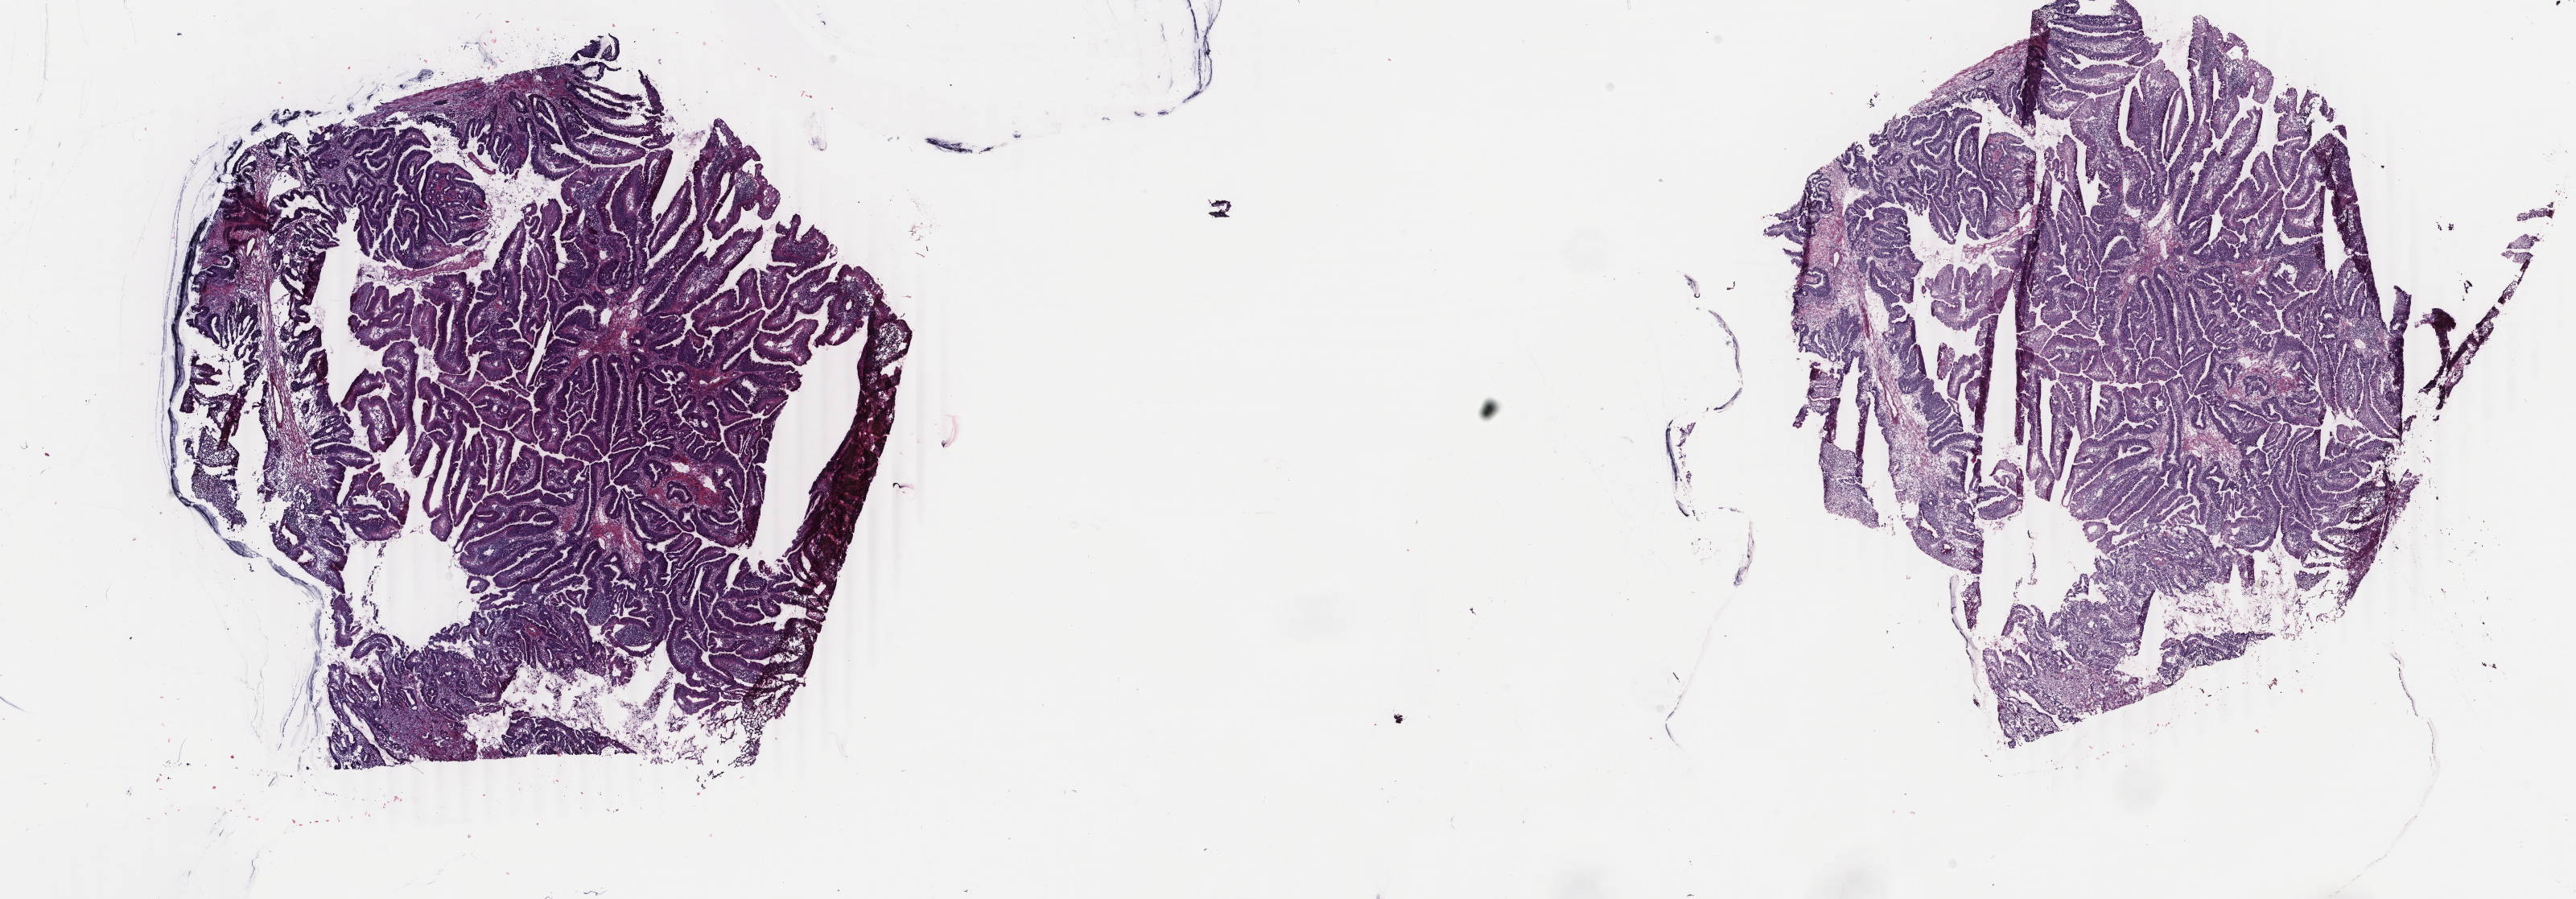
Whole-slide histology image, H&E-stained — low-resolution overview of the scanned area, about 25.5 x 8.9 mm (acquisition: 40x scan), frozen section, colon, primary tumour sample. Patient sex: female. Pathologist review of this section (percent, as recorded): tumour cells 75%, tumour nuclei 75%, normal cells 0%, stromal cells 25%, necrosis 0%. Inflammatory infiltration, as recorded: lymphocyte infiltration 3%, monocyte infiltration 0%, neutrophil infiltration 1%.
Diagnosis: Mucinous adenocarcinoma (cecum). Lymph nodes positive (case pathology): 4 of 29 examined. AJCC pathologic stage: III (5th edition).